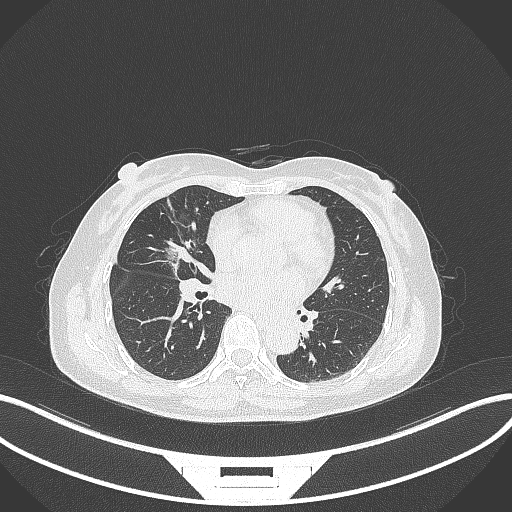
Chest CT, one axial slice; position 141 of 284 along the scan axis; 120 kVp; lung window (W 1500 / L -600 HU); 1 mm slice thickness; 512 × 512 image matrix, field of view 400 × 400 mm. Patient: female, 51 years. From the clinical record (not read from this slice): clinical TNM (as recorded): T1c N0 M0; histopathological grade: G2.
Annotated regions visible in this slice (rectangle marked by the reading radiologist):
- lung tumour (recorded histology: adenocarcinoma): box from (x=161, y=236) to (x=193, y=270) px